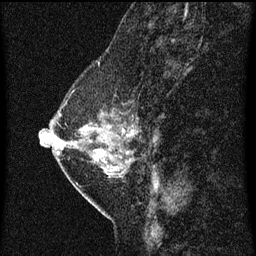
Breast MRI (dynamic contrast-enhanced), one sagittal slice; slice 22 of 60 in the series (ordered by position); dynamic contrast-enhanced series, image 2 of 3 at this slice position (ordered by acquisition); 1.5 T; TE 4.2 ms, TR 8 ms; 2 mm slice thickness; 256 × 256 image matrix, field of view 180 × 180 mm. Female patient, age 47 years.
Annotated regions visible in this slice (semi-automatic segmentation, software-assisted and operator-edited):
- analysis volume of interest (the breast-tissue region the enhancement analysis was run in; not a lesion): box from (x=54, y=86) to (x=142, y=187) px
- tumour enhancement mask (voxels above the 70 % enhancement threshold inside the analysis volume of interest): (x=59, y=130)–(x=135, y=163)